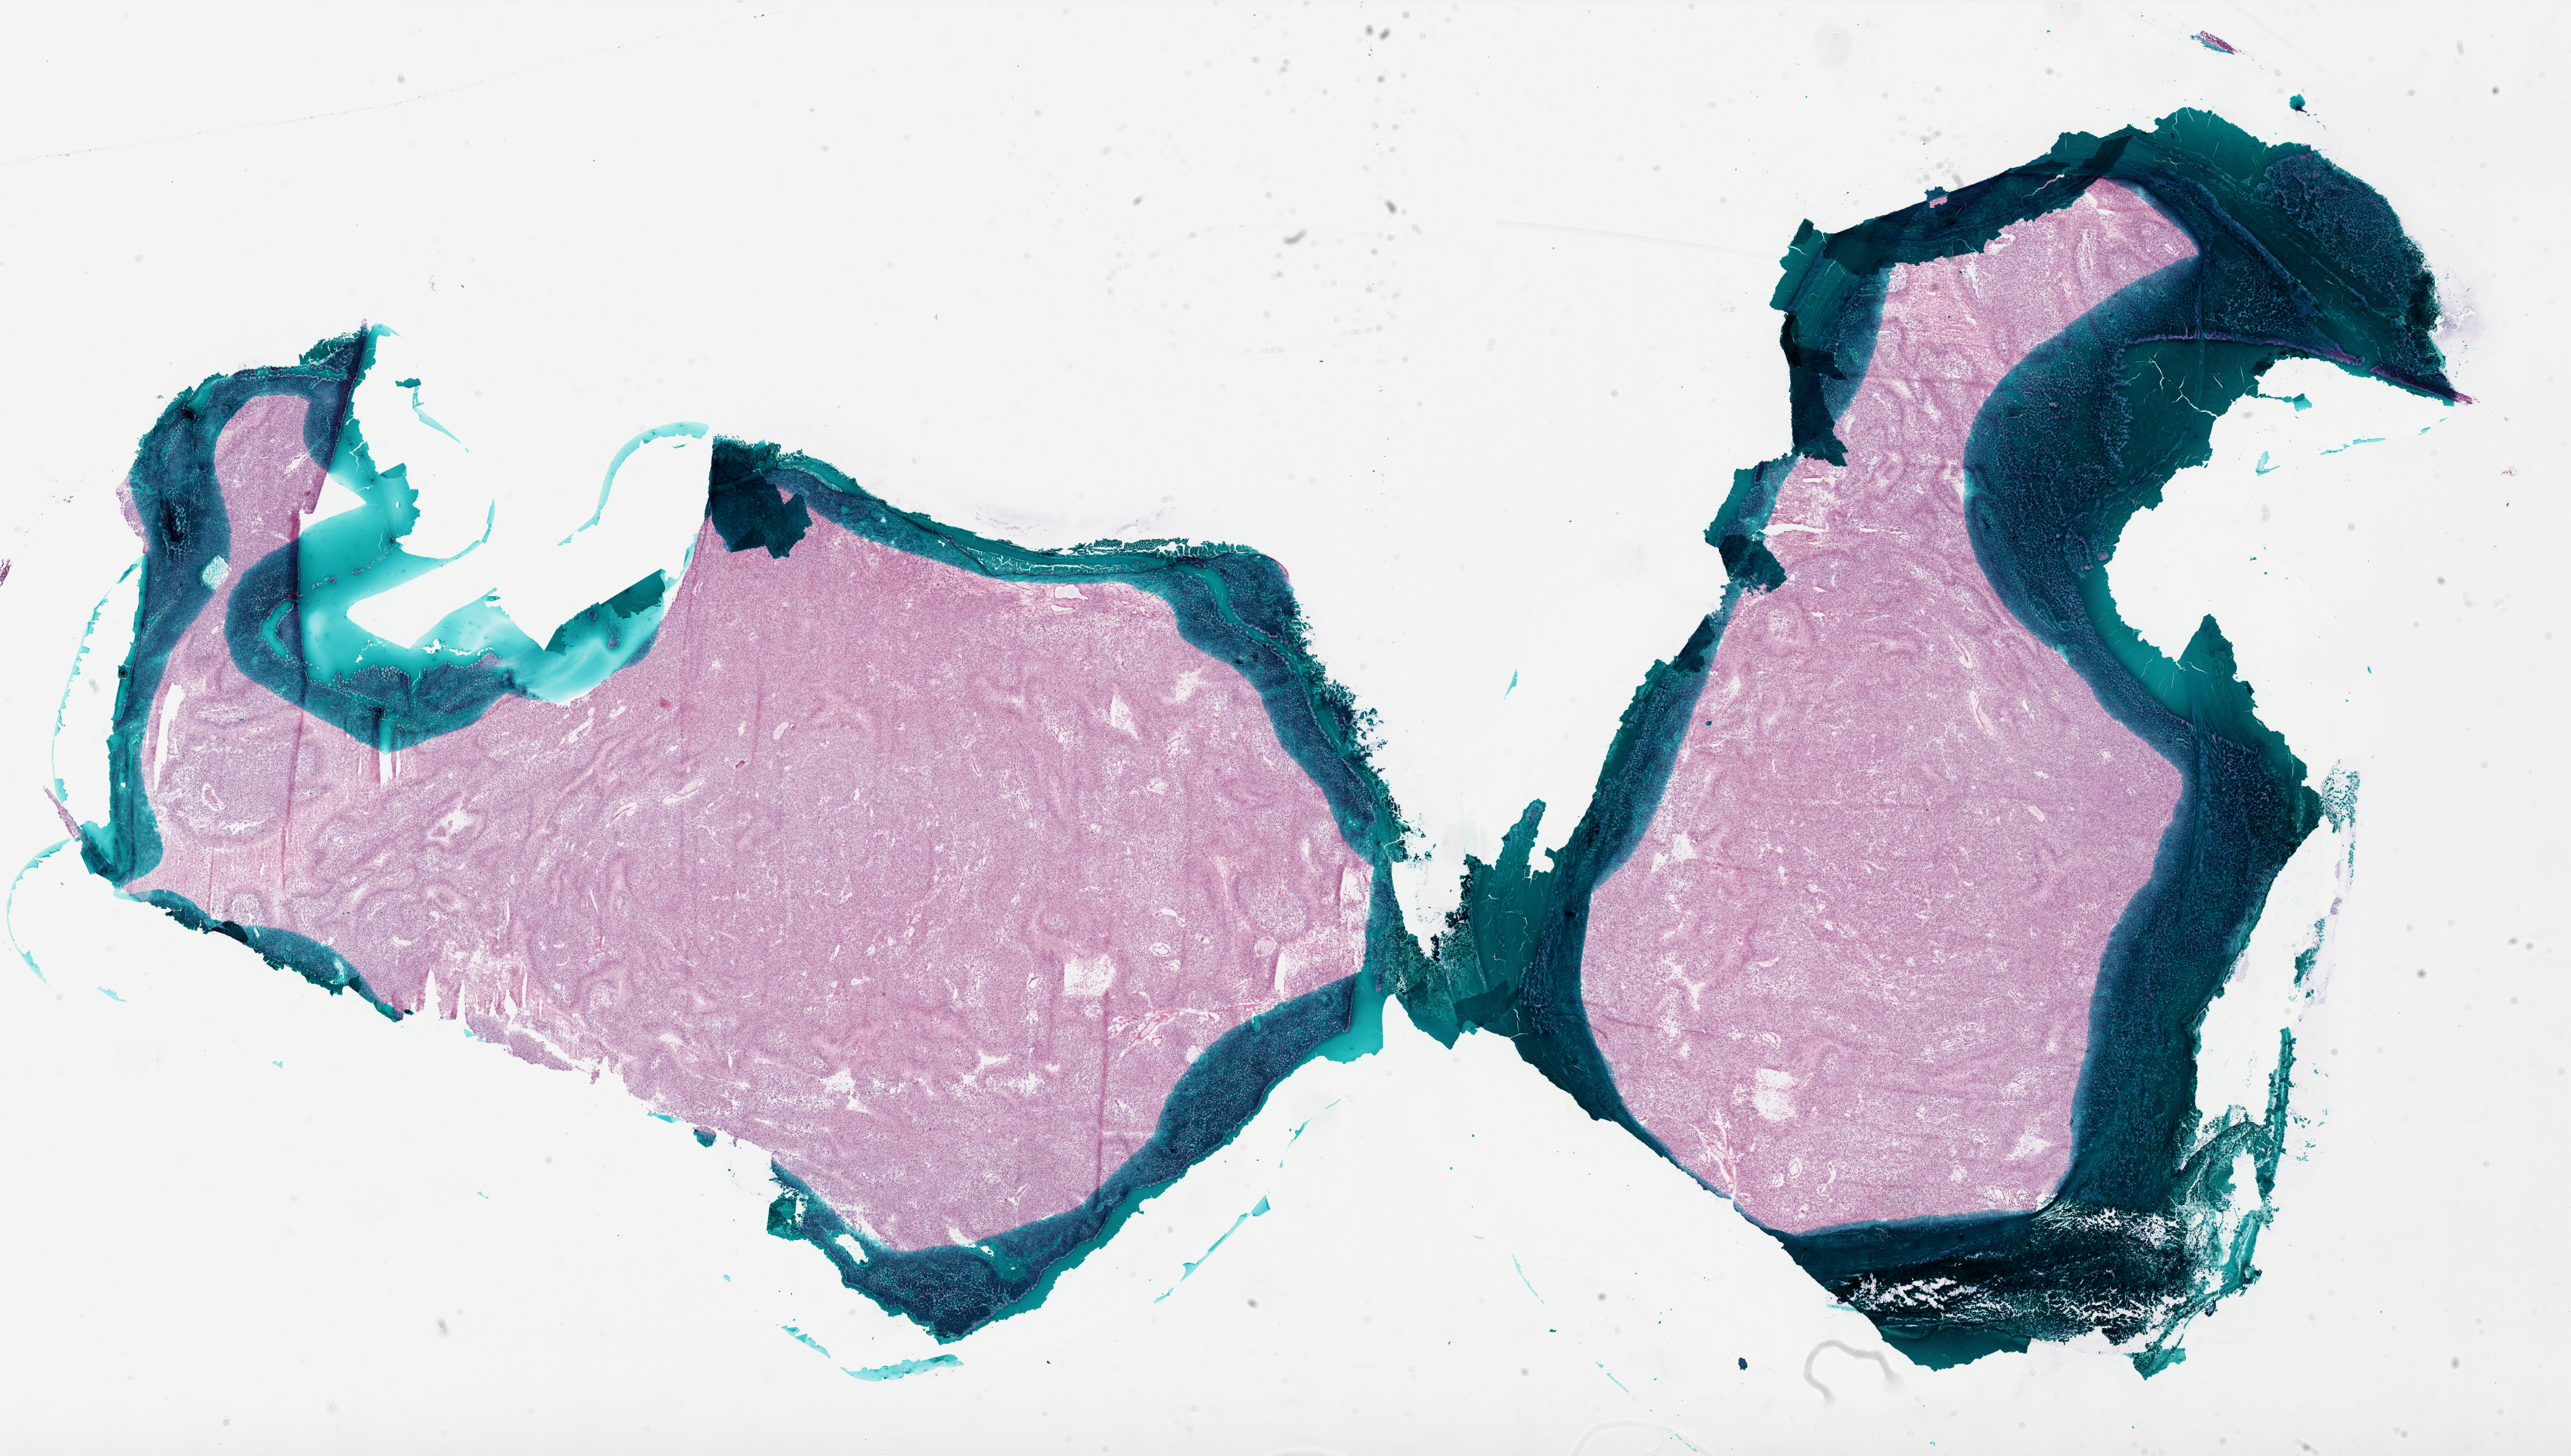
Whole-slide histology image, H&E, a low-resolution overview of the entire scanned area, about 33.0 x 18.7 mm (from a 20x scan); frozen section from the bottom of the tissue portion; sample: primary tumour, brain. Patient: female, age at initial diagnosis 54 years. Composition of this section per pathologist review: tumour cells 80%, tumour nuclei 100%, normal cells 0%, stromal cells 0%, necrosis 20%.
• diagnosis: Glioblastoma